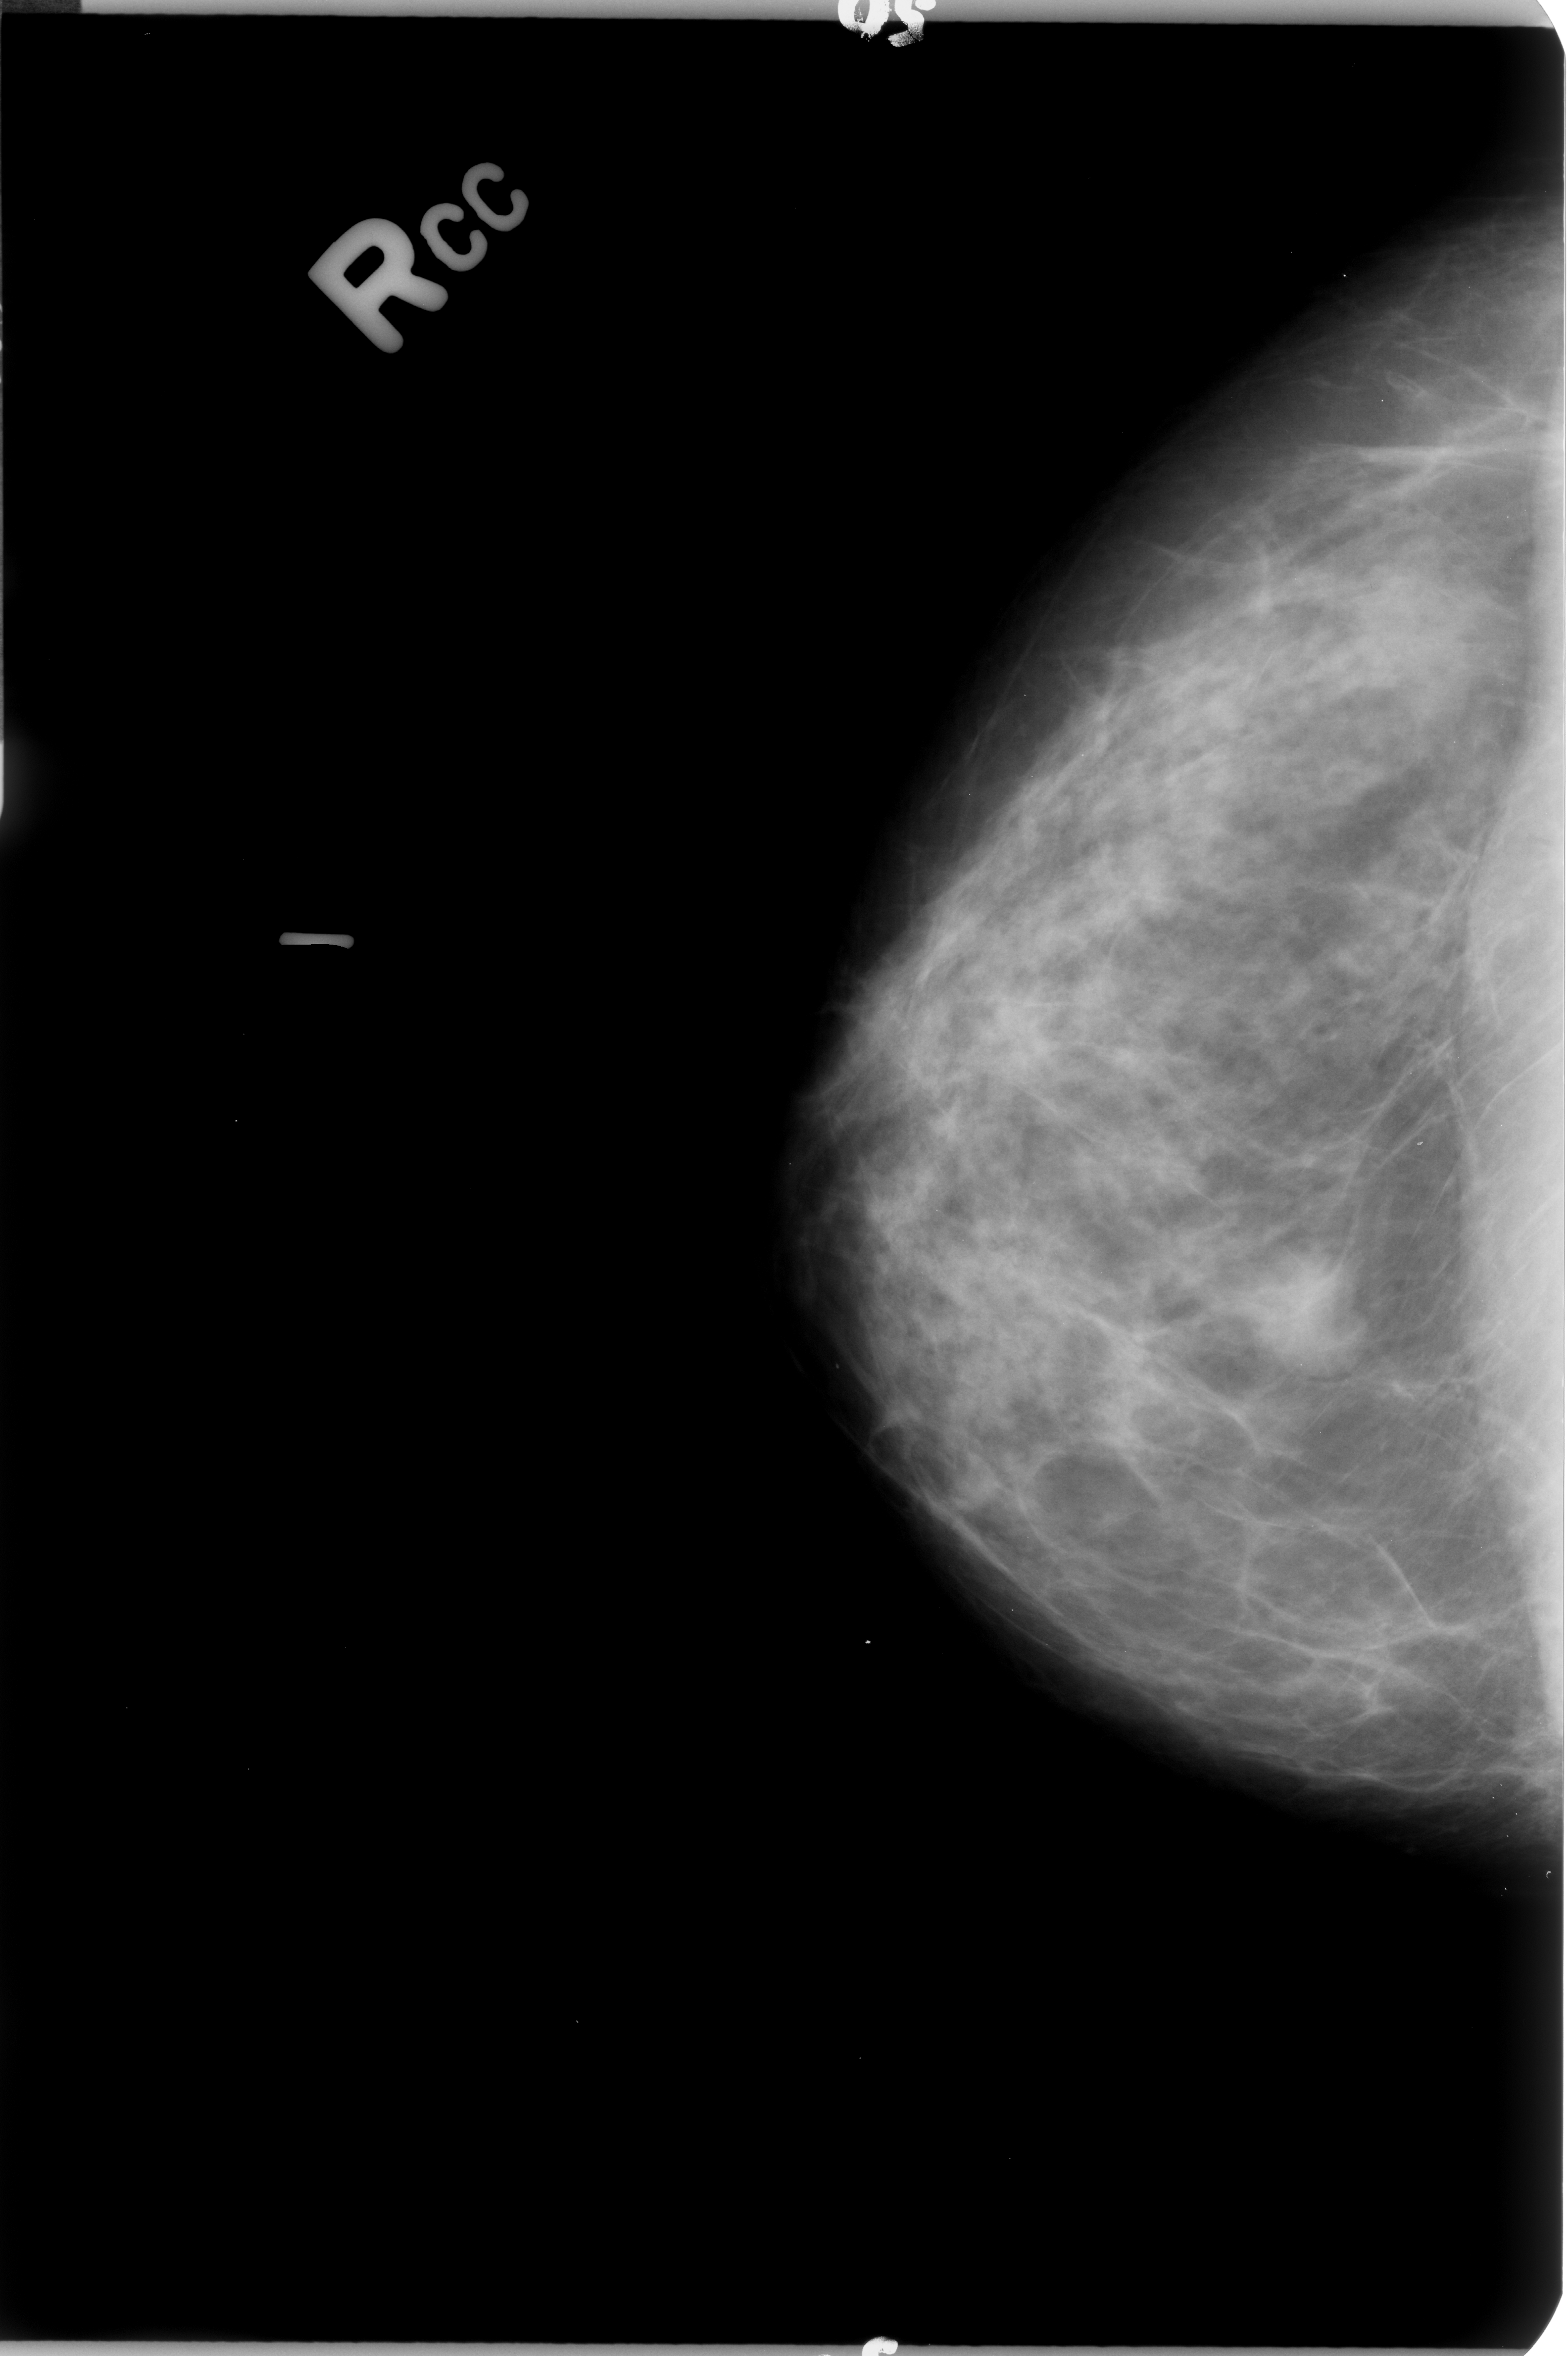
Mammogram (digitized film), right breast, craniocaudal (CC) view, BI-RADS breast density category 3 (scale 1–4).
Mass, shape lobulated, margins circumscribed / ill defined; BI-RADS assessment category 4; subtlety rating 4 on a 1 (subtle) to 5 (obvious) scale; pathology (as recorded): benign.